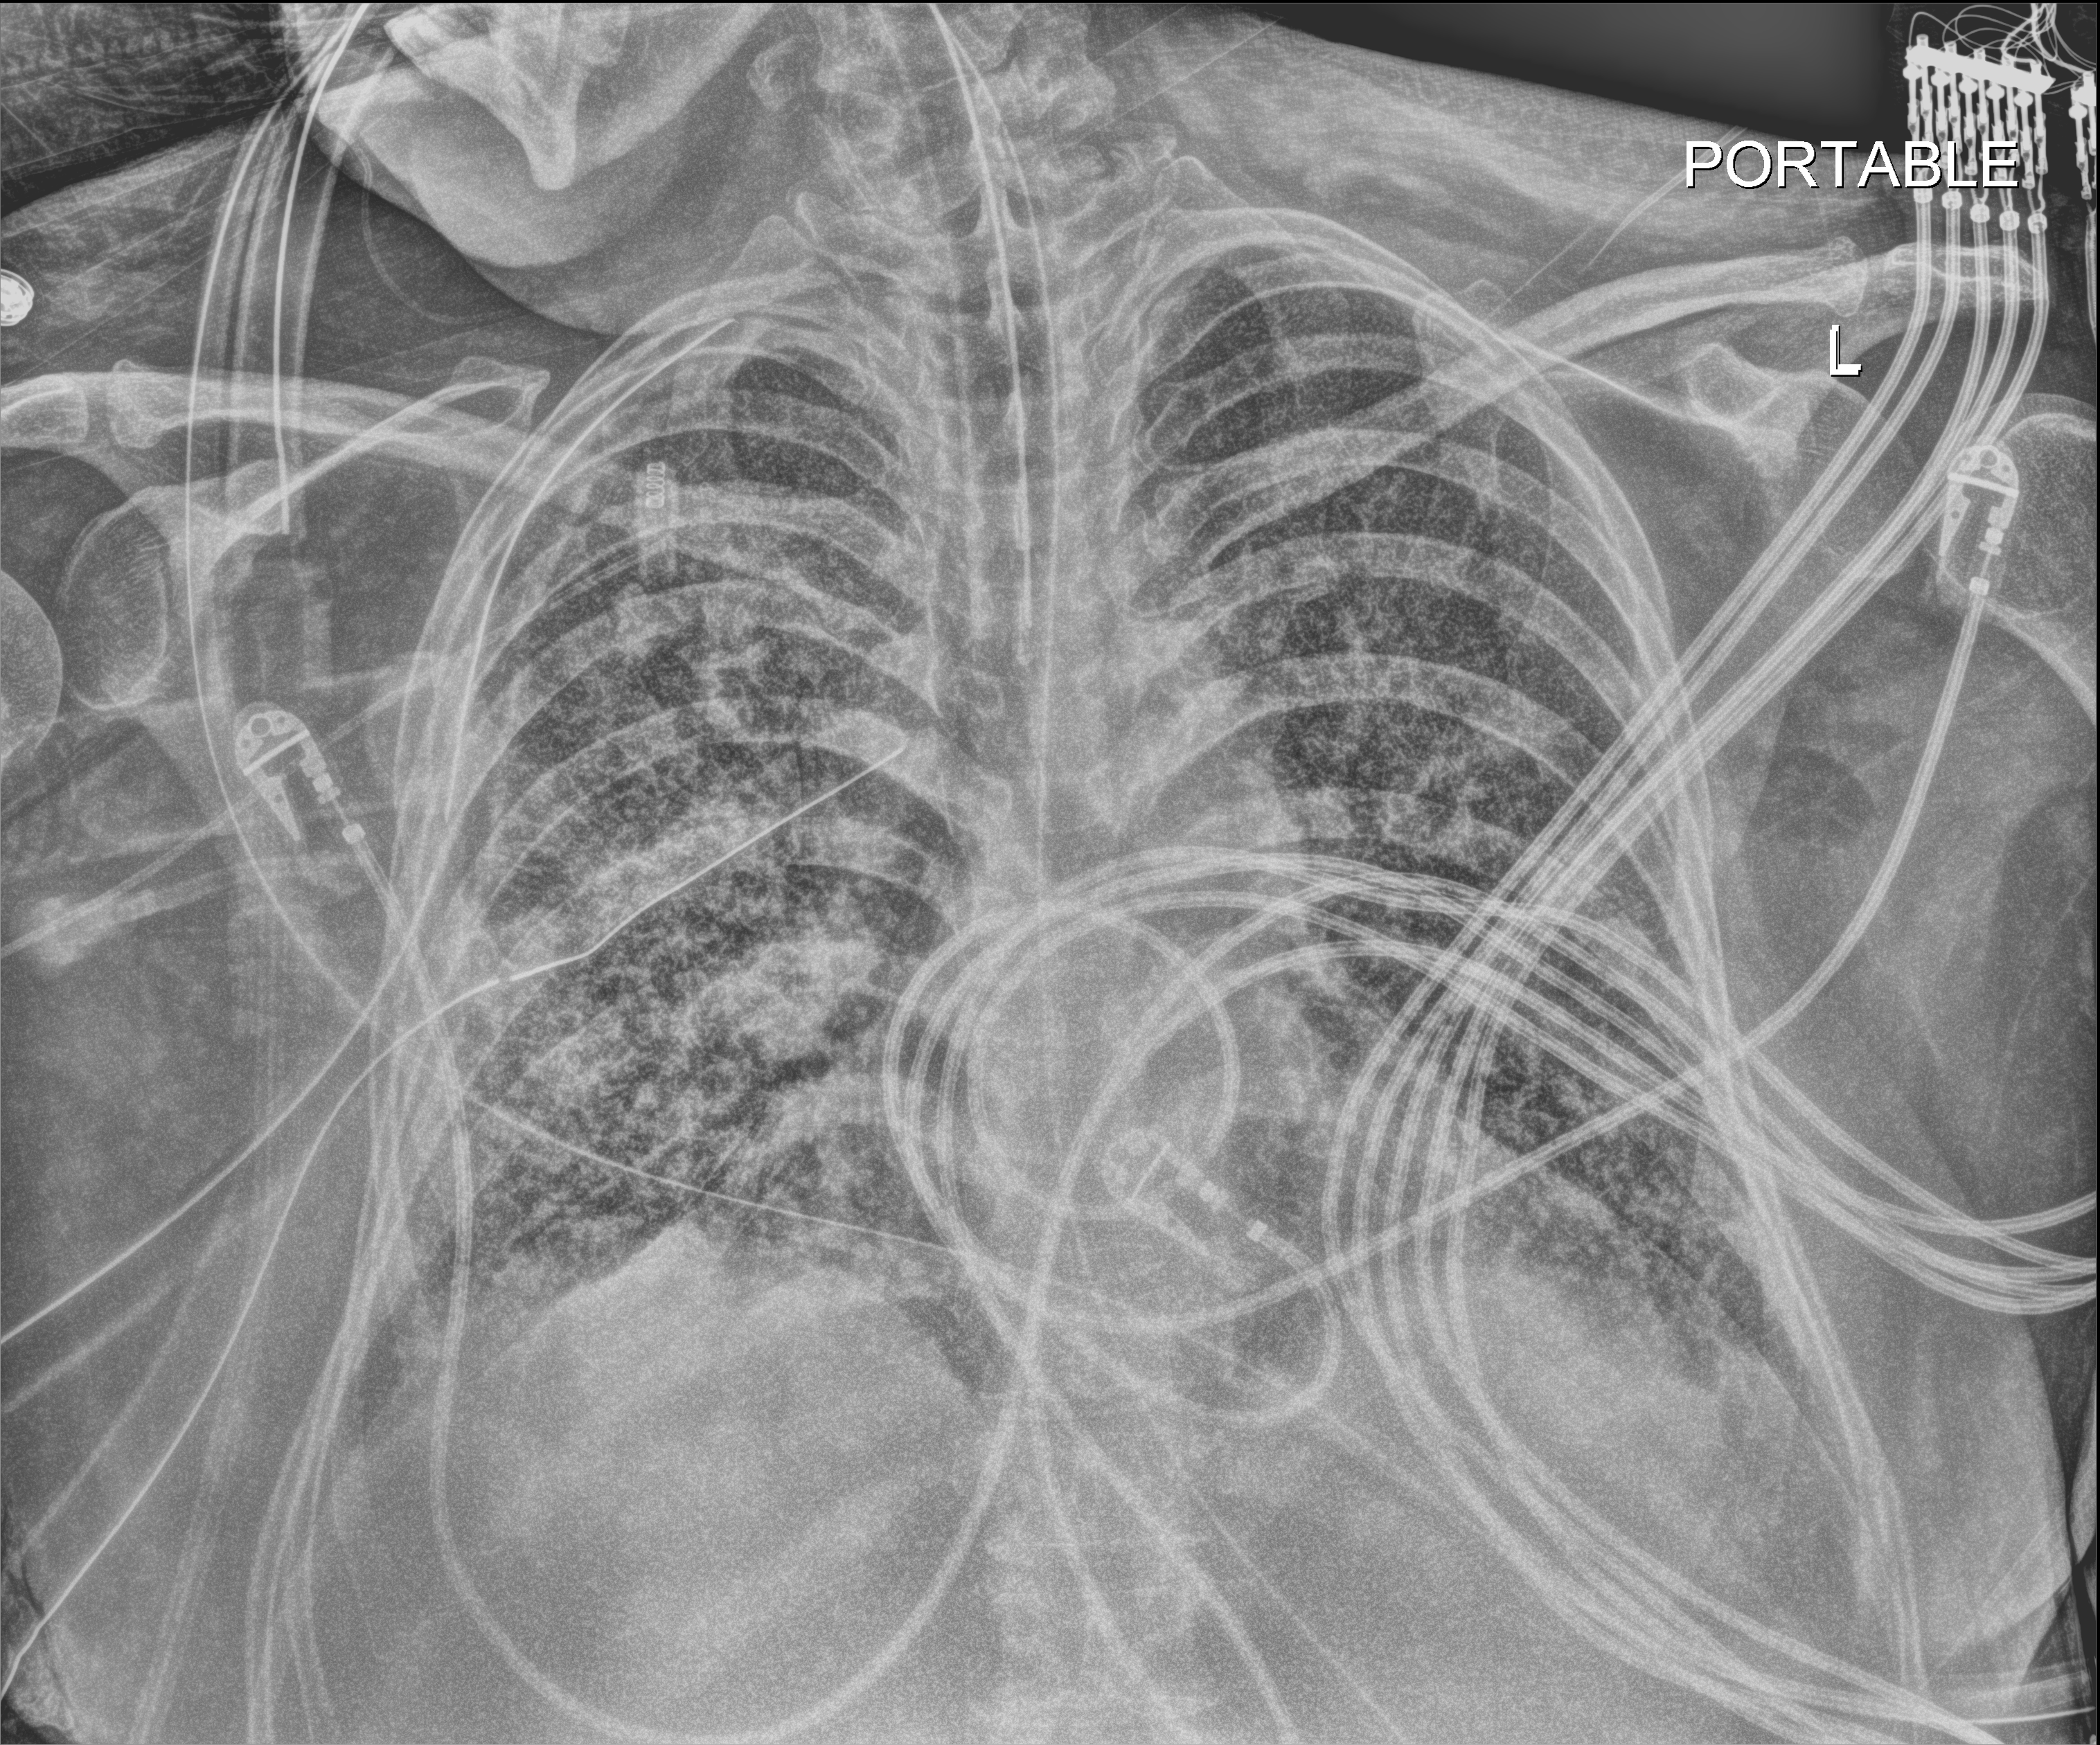
Portable chest radiograph, anteroposterior (AP) projection. Patient hospitalised with COVID-19, aged 18–59 years.
From the hospital-stay record, not from the radiograph (when in the stay this image was taken is not recorded): mechanically ventilated during this hospital stay: yes.